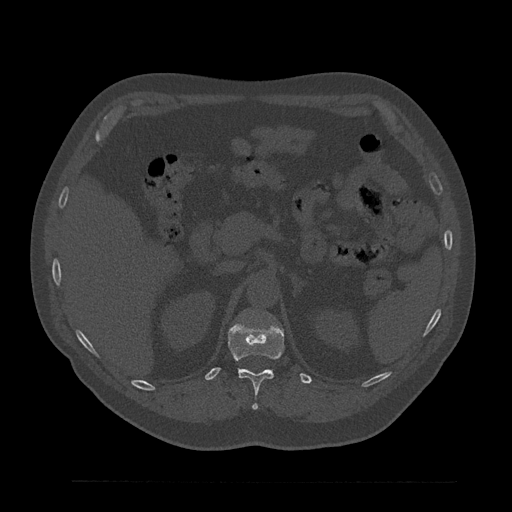
CT including the spine, one axial slice. Position 220 of 797 along the scan axis. Reconstruction kernel Br40s/3. 120 kVp. Bone window (W 1800 / L 400 HU). 512 × 512 image matrix, field of view 430 × 430 mm. Male patient, age 61 years. Case-level facts recorded for this patient, not image findings: primary cancer: prostate.
Structures marked on this image (semi-automatic segmentation, software-assisted and operator-edited):
- T12 vertebra: bounding box <228,322,284,410> (left, top, right, bottom; pixels)